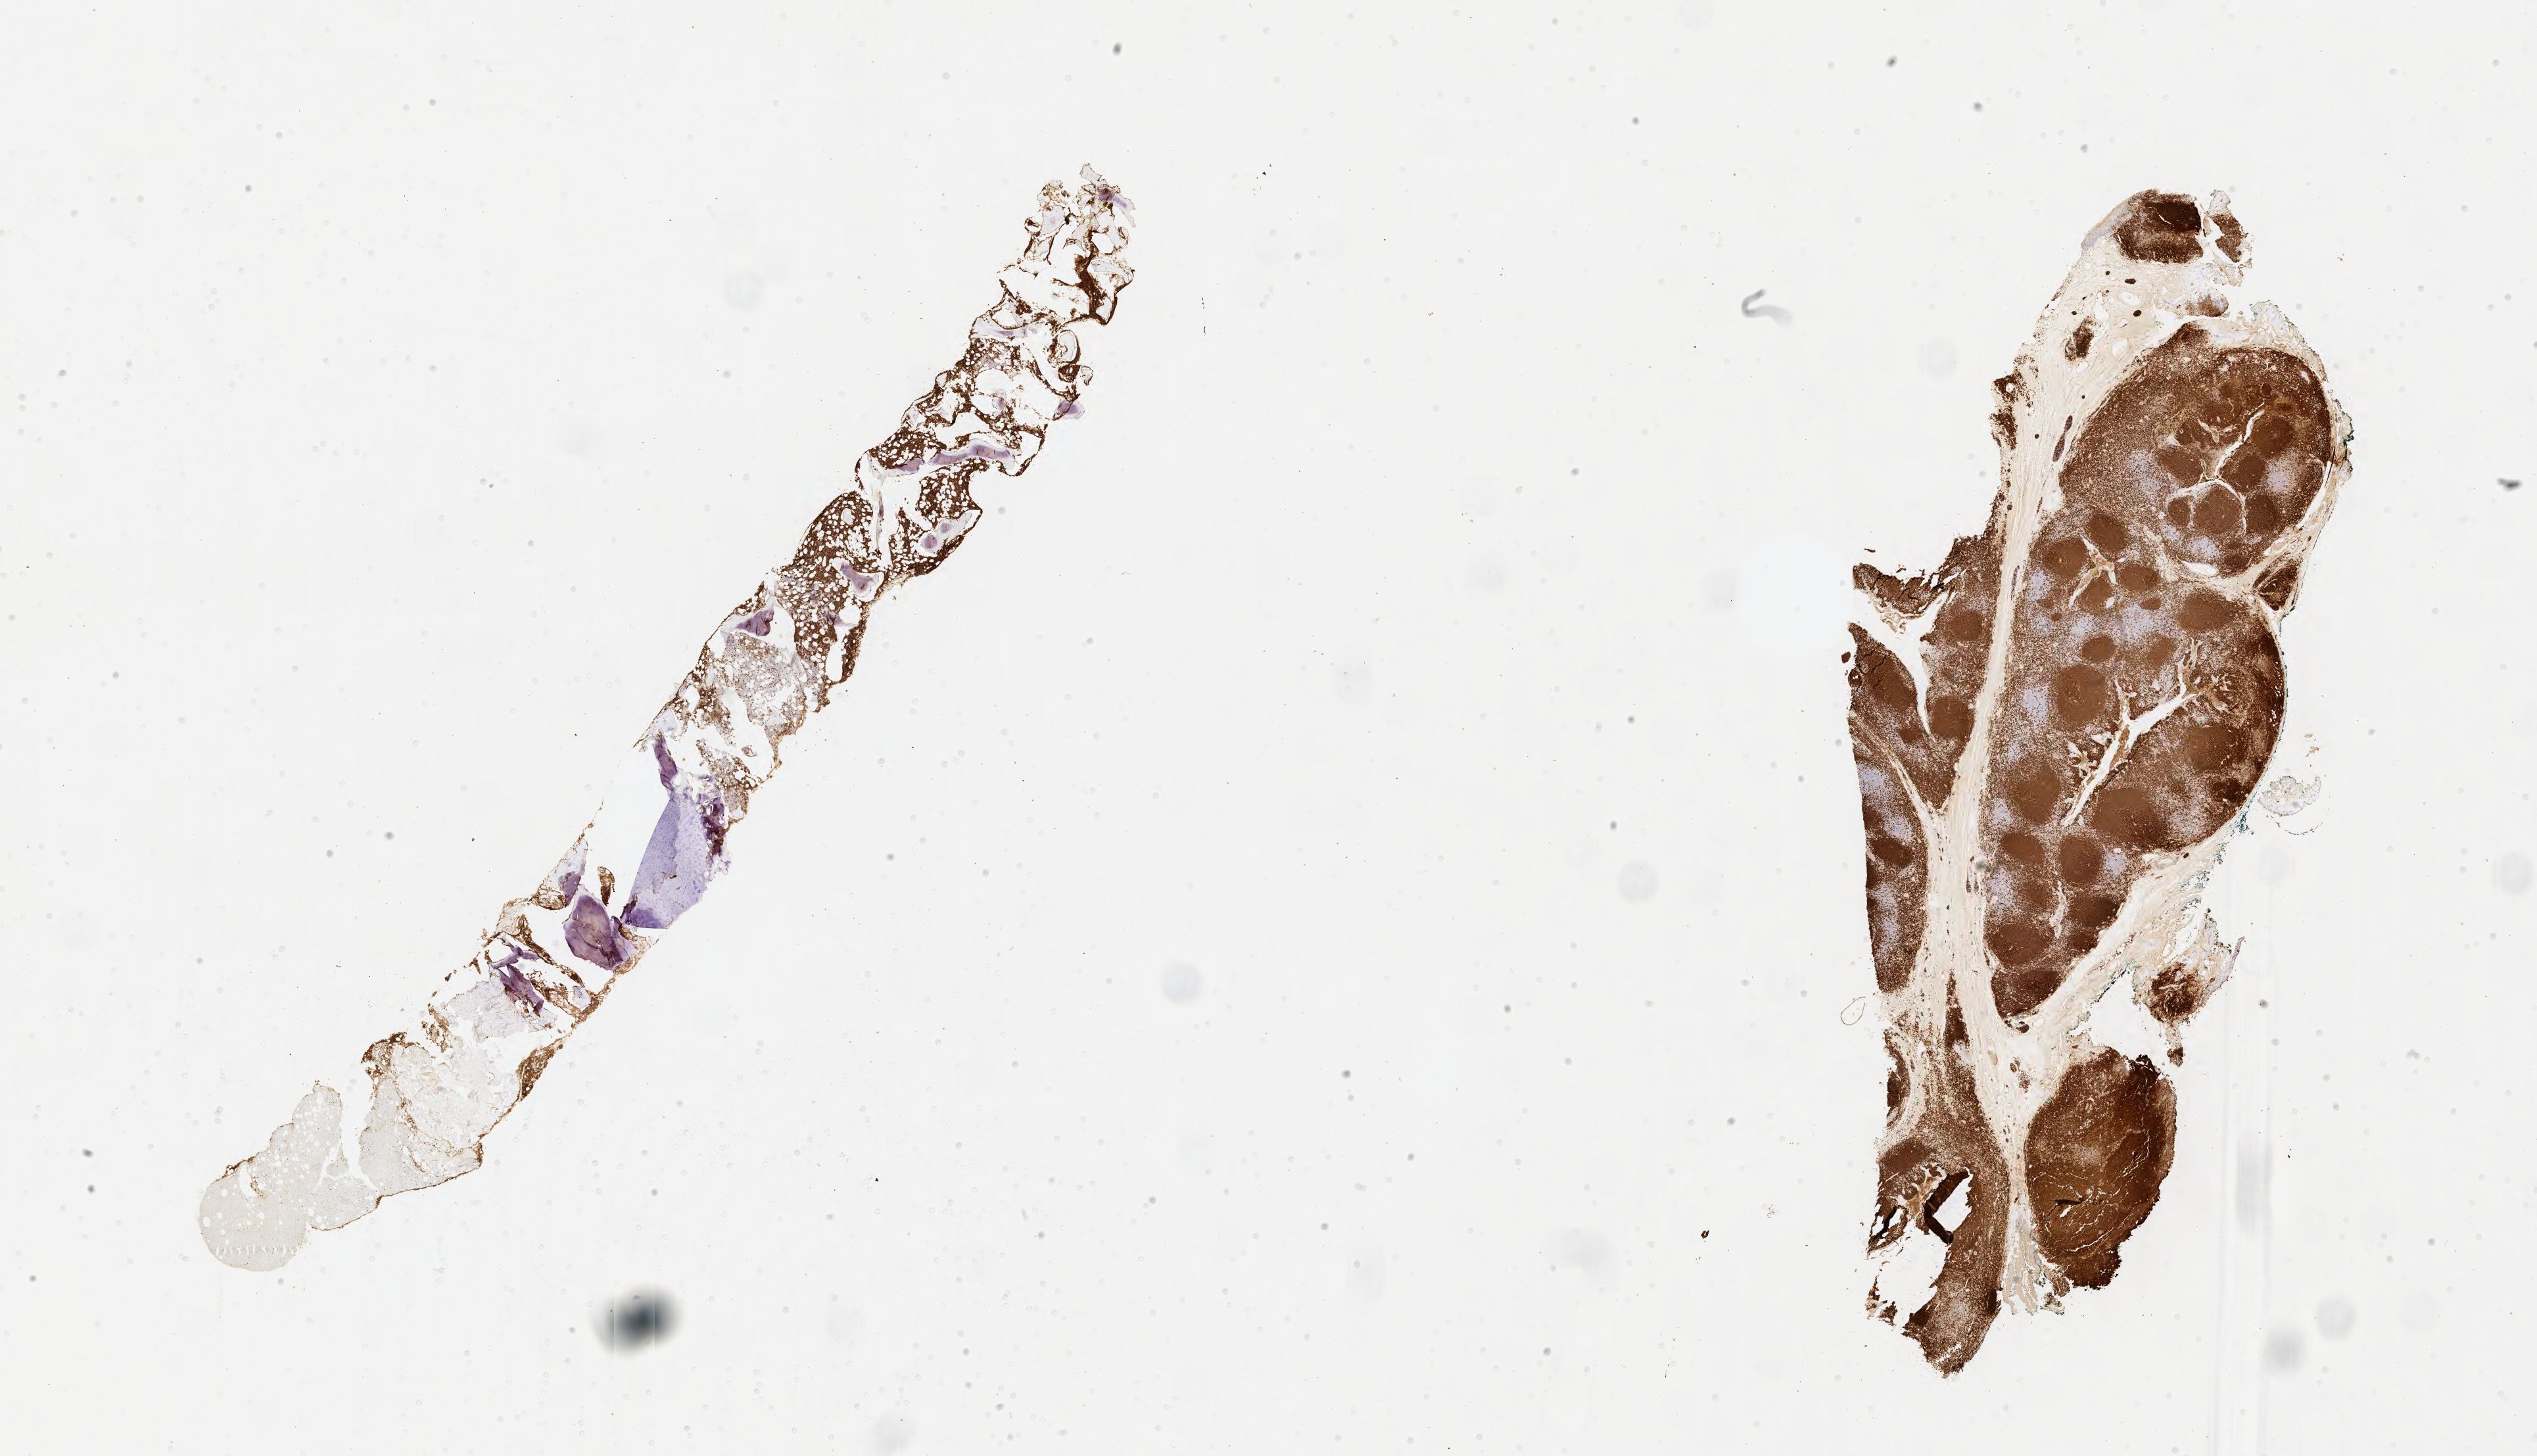
IHC for CD20, whole-slide image — shown as a low-resolution overview of the whole scanned area (about 31.2 x 17.9 mm), specimen: tumor tissue, site: bone marrow. Patient: male, aged 15.
Diagnosis: Burkitt lymphoma, NOS.